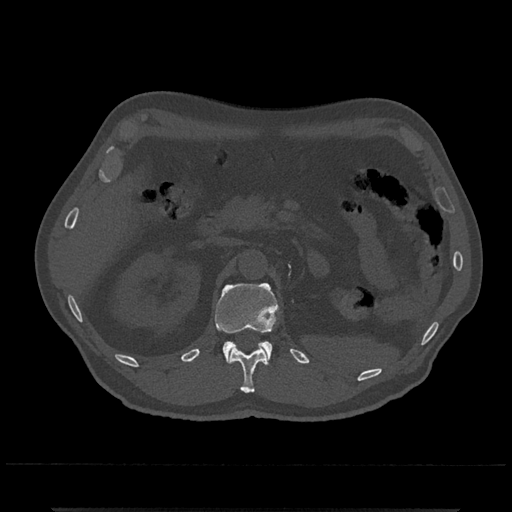
CT including the spine, one axial slice. Position 395 of 797 along the scan axis. 120 kVp. Bone window (W 1800 / L 400 HU). 512 × 512 image matrix. Male patient, age 67 years. Case-level facts recorded for this patient, not image findings: primary cancer: prostate.
Outlined on this slice (semi-automatically segmented with operator editing):
- L1 vertebra: bounding box [x1, y1, x2, y2] px = [214, 283, 279, 364]
- T12 vertebra: [230, 346, 268, 393]